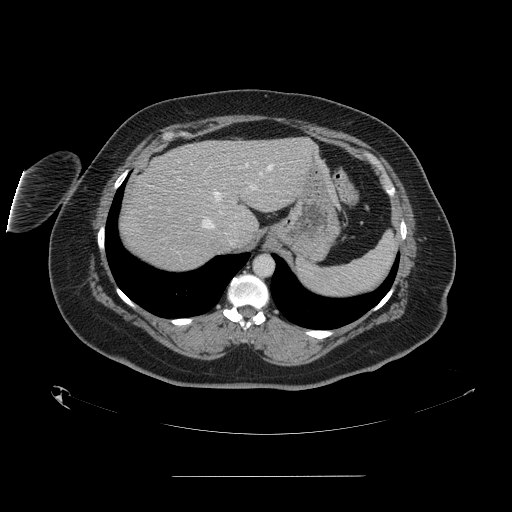
Contrast-enhanced abdominal CT, one axial slice. Position 120 of 164 along the scan axis. 120 kVp. Intravenous contrast given. Soft-tissue window (W 400 / L 40 HU). 2.5 mm slice thickness. 512 × 512 image matrix, field of view 495 × 495 mm. Female patient, age 52 years. From the clinical record (not read from this slice): diagnosis: colorectal cancer liver metastases, imaged before liver resection; multiple liver metastases: yes; largest metastasis: 3.5 cm; chemotherapy before resection: no.
Annotated regions visible in this slice (outlined manually by an expert reader):
- hepatic veins: bounding box <202,163,273,228> (left, top, right, bottom; pixels)
- liver: <119,138,313,271>
- planned liver remnant (the part of the liver to remain after resection): <169,138,313,225>
- portal vein (with intrahepatic branches): <177,177,254,213>